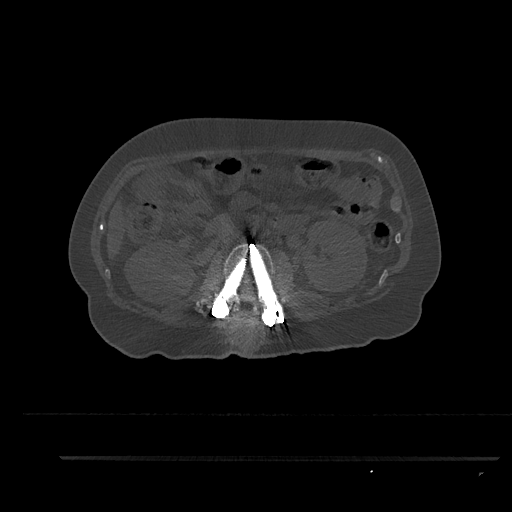
CT including the spine, one axial slice; position 170 of 797 along the scan axis; reconstruction kernel Br40s/3; 120 kVp; bone window (W 1800 / L 400 HU); 512 × 512 image matrix, field of view 408 × 408 mm. Female patient, age 44 years. From the clinical record (not read from this slice): primary cancer: renal; vertebrae with lytic lesions (as recorded): L1.
Annotated regions visible in this slice (semi-automatically segmented with operator editing):
- L2 vertebra: box from (x=209, y=243) to (x=284, y=319) px